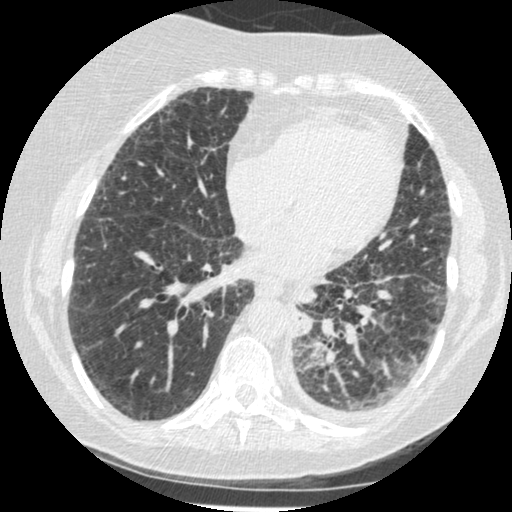
Low-dose screening chest CT, one axial slice. Reconstruction kernel STANDARD. 120 kVp. Lung window (W 1500 / L -600 HU). 1.25 mm slice thickness. 512 × 512 image matrix, field of view 310 × 310 mm.
Outlined on this slice (outlined manually by an expert reader):
- lesion 1 (tumor, lower lobe of left lung): bounding box <294,323,311,336> (left, top, right, bottom; pixels)